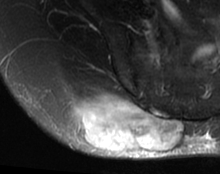
MRI of an extremity soft-tissue mass, one axial slice. Slice 39 of 63 in the series (ordered by position). T2-weighted fat-saturated. MR volume resampled by the dataset authors to the PET/CT grid (not the native acquisition matrix). 3.27 mm slice thickness. 220 × 174 image matrix, field of view 215 × 170 mm. Female patient. Case-level facts recorded for this patient, not image findings: histological type: spindle cell suggestive of myxofibrosarcoma; grade: intermediate; site of the primary tumour: right buttock.
Outlined on this slice (expert contour drawn on MRI and transferred to this co-registered scan by the dataset authors):
- gross tumour volume (mass): bounding box (x1, y1, x2, y2) in pixels: (70, 93, 183, 153)